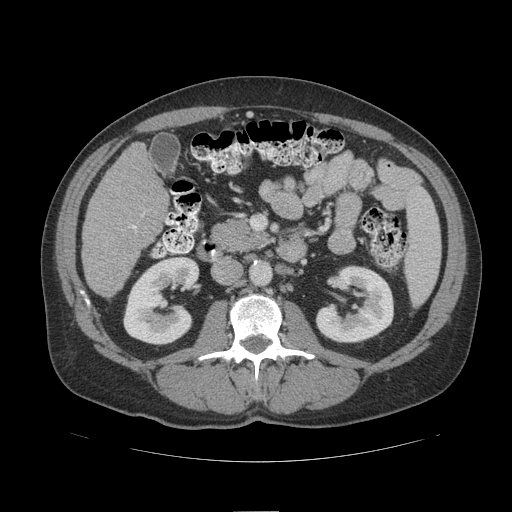
Contrast-enhanced abdominal CT (liver protocol), one axial slice. Position 41 of 109 along the scan axis. Reconstruction kernel STANDARD. Soft-tissue window (W 400 / L 40 HU). 512 × 512 image matrix, field of view 420 × 420 mm. Case-level facts recorded for this patient, not image findings: diagnosis: hepatocellular carcinoma (patient treated with transarterial chemoembolisation; whether this scan precedes or follows treatment is not stated here); TNM stage (as recorded): Stage-IIIB; Child-Pugh class: A; tumour nodularity: multinodular.
Structures marked on this image (semi-automatically segmented with operator editing):
- liver parenchyma outside the tumour (the mass and vessels are separate outlines, so this box may not span the whole liver): box from (x=82, y=142) to (x=168, y=296) px
- liver vessels: (x=132, y=214)–(x=144, y=229)